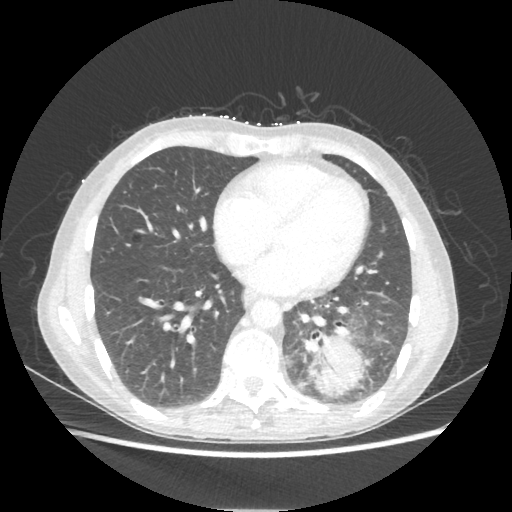
Chest CT, one axial slice; slice 87 of 221 in the series (ordered by position); reconstruction kernel STANDARD; 80 kVp; lung window (W 1500 / L -600 HU); 1.25 mm slice thickness; 512 × 512 image matrix, field of view 360 × 360 mm. Female patient, age 53 years. Case-level facts recorded for this patient, not image findings: clinical TNM (as recorded): T3 N0 M0.
Outlined on this slice (bounding box drawn by a radiologist):
- lung tumour (recorded histology: adenocarcinoma): box from (x=305, y=333) to (x=366, y=398) px